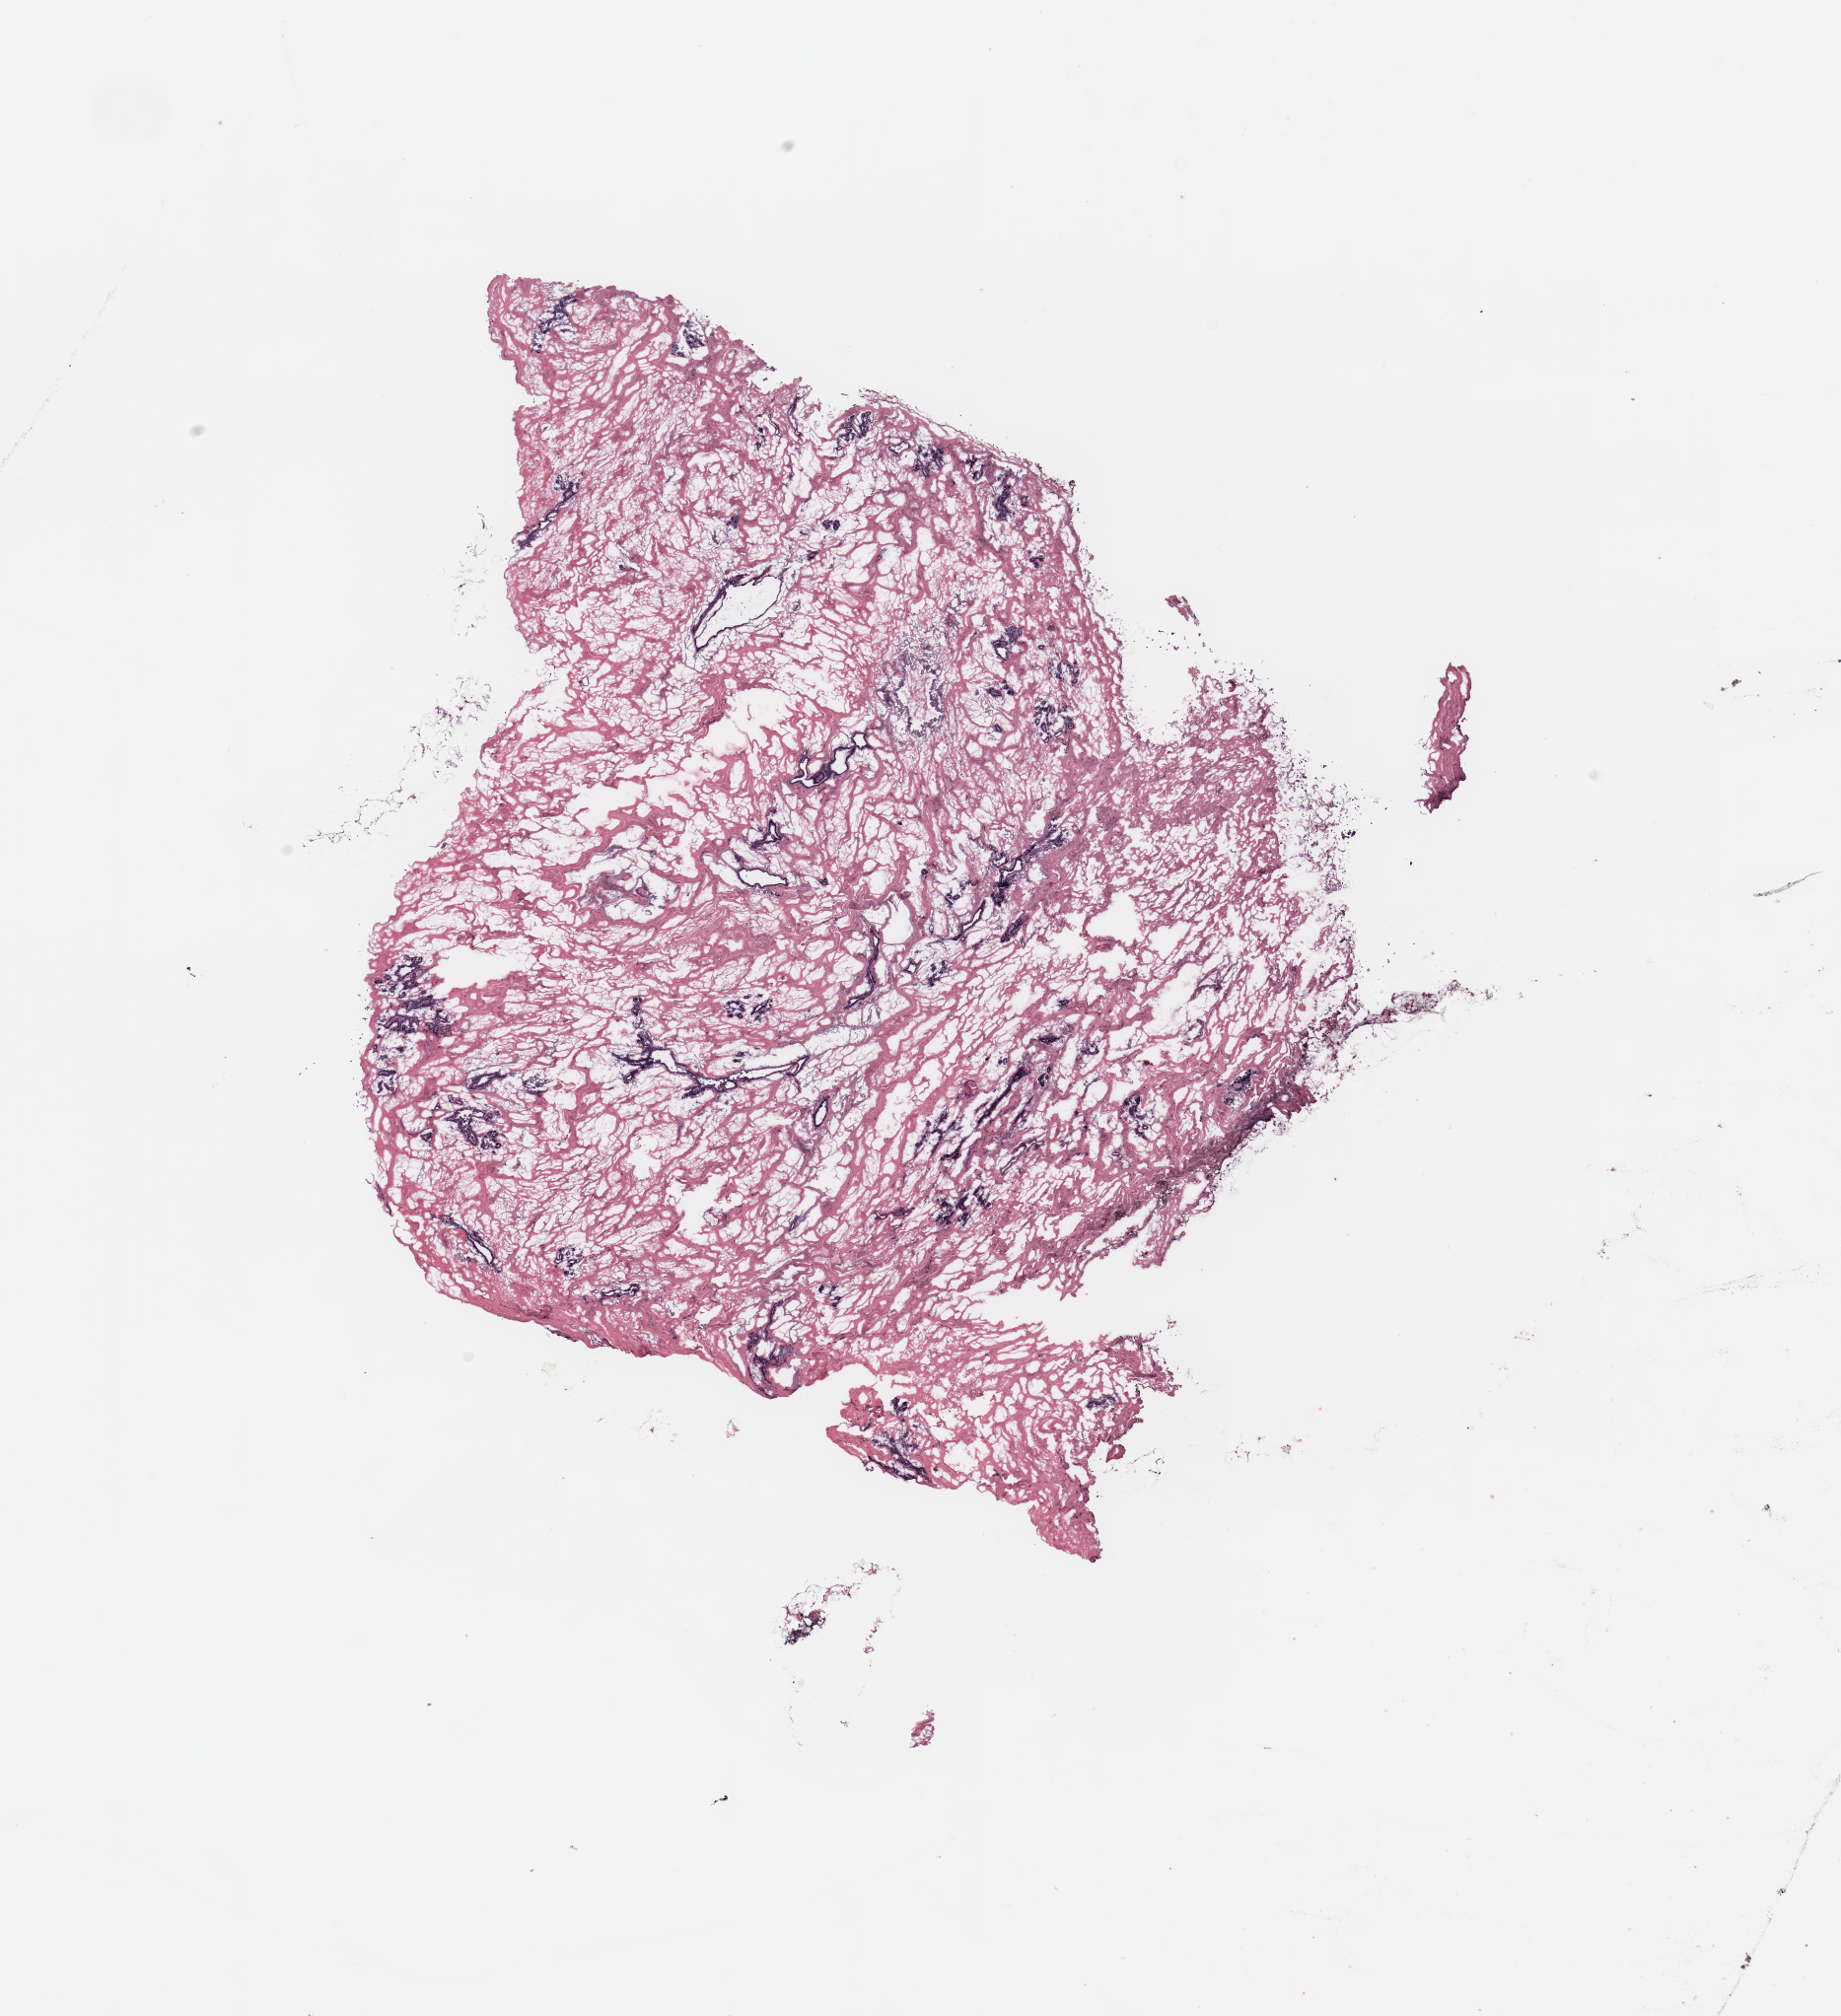
H&E whole-slide image — whole scanned area (about 14.8 x 16.2 mm, from a 20x scan) shown as a low-resolution overview, tumour tissue sample, breast. 71-year-old female patient.
- AJCC pathologic stage: IIA
- diagnosis: Infiltrating duct carcinoma, NOS